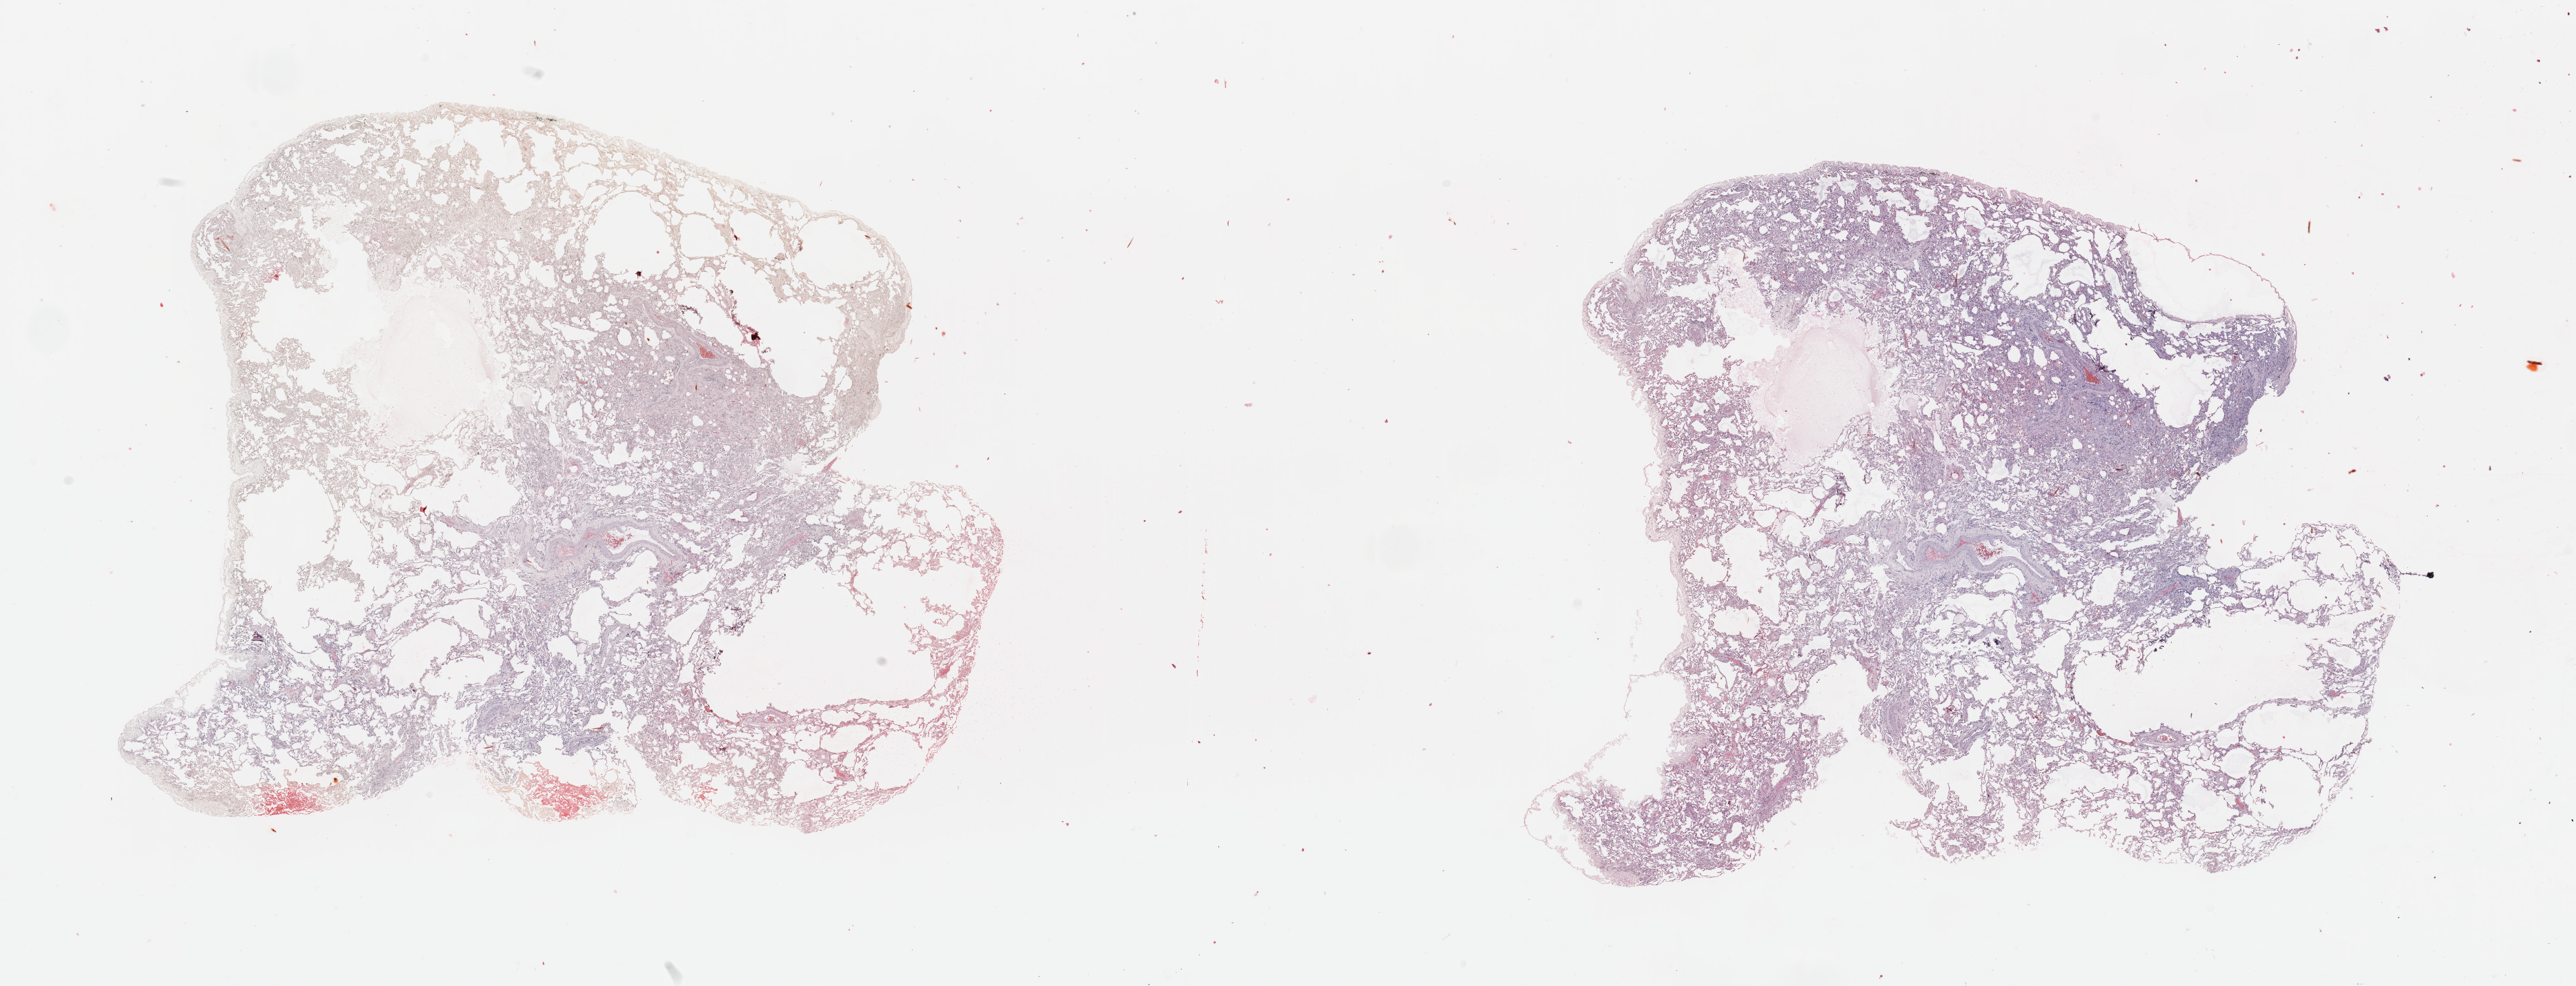
Hematoxylin and eosin (H&E) stained whole-slide image — low-resolution overview of the scanned area, about 29.5 x 11.3 mm. Normal (non-tumour) tissue sample, sampled site: lung. Patient: female, age 48 years.
This section: normal (non-tumour) tissue from the same patient. Patient diagnosis: Squamous cell carcinoma, NOS.